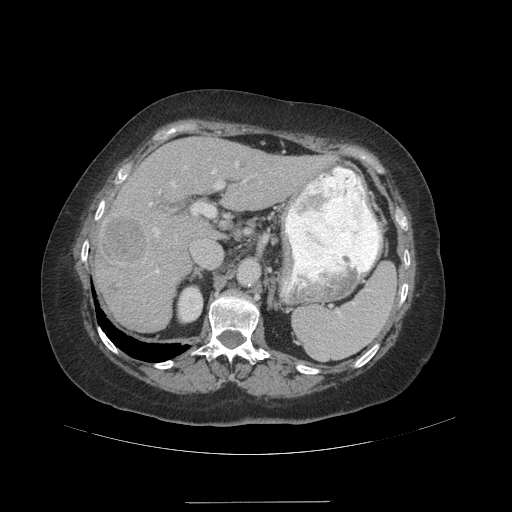
Contrast-enhanced abdominal CT (liver protocol), one axial slice; slice 66 of 99 in the series (ordered by position); reconstruction kernel STANDARD; 140 kVp; soft-tissue window (W 400 / L 40 HU); 512 × 512 image matrix, field of view 440 × 440 mm. From the clinical record (not read from this slice): diagnosis: hepatocellular carcinoma (patient treated with transarterial chemoembolisation; whether this scan precedes or follows treatment is not stated here); TNM stage (as recorded): Stage-IVA; Child-Pugh class: A; tumour nodularity: multinodular.
Outlined on this slice (semi-automatically segmented with operator editing):
- liver parenchyma outside the tumour (the mass and vessels are separate outlines, so this box may not span the whole liver): bounding box <94,138,324,330> (left, top, right, bottom; pixels)
- mass: <101,216,148,297>
- liver vessels: <149,163,246,273>